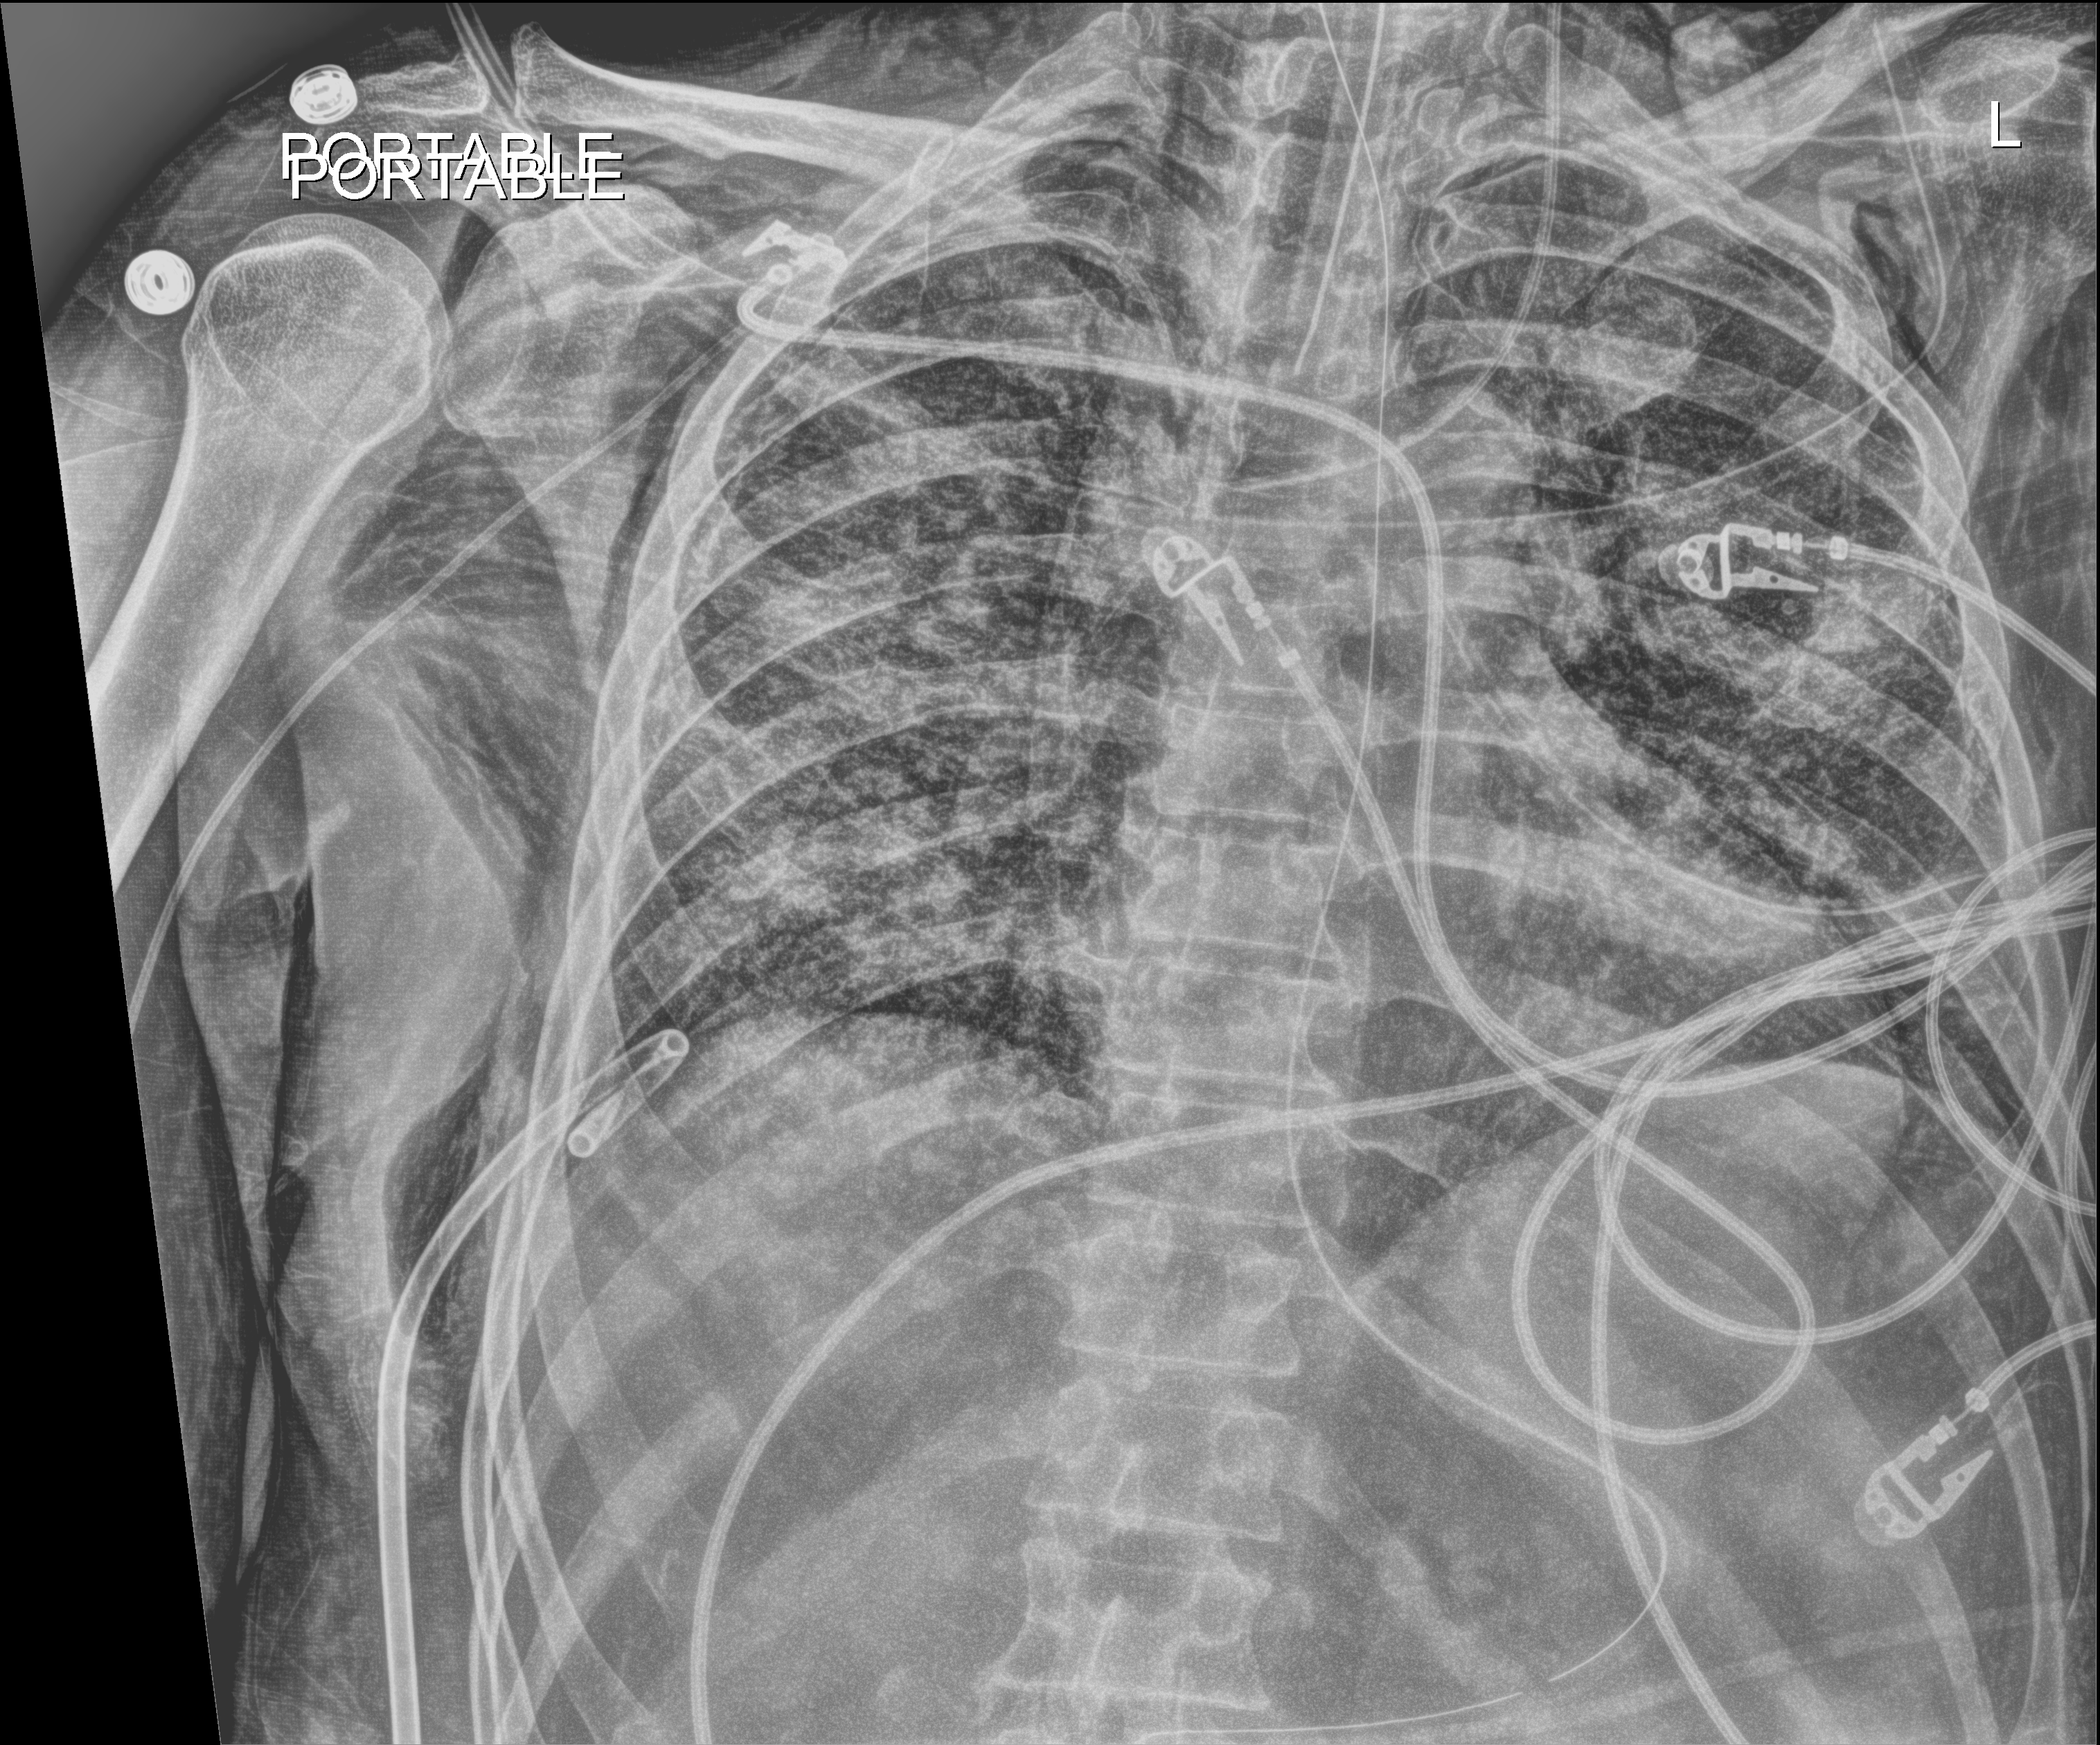
Portable chest radiograph, anteroposterior (AP) projection. Male patient hospitalised with COVID-19, age 18–59 years.
Hospital-stay facts (about this admission, not read from this image; timing relative to this image not recorded): admitted to intensive care during this hospital stay: yes; mechanically ventilated during this hospital stay: yes.